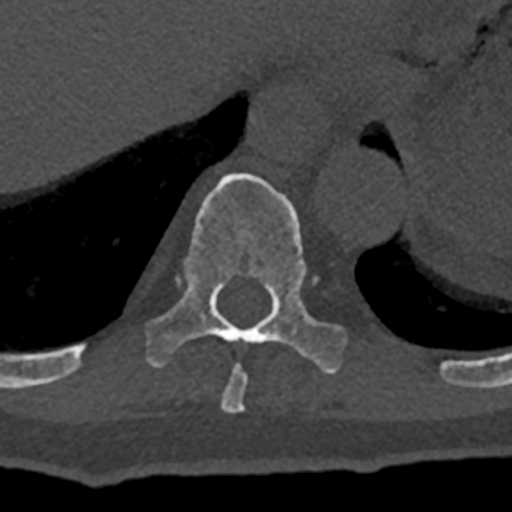
CT including the spine, one axial slice; slice 608 of 797 in the series (ordered by position); reconstruction kernel Br40s/3; 120 kVp; bone window (W 1800 / L 400 HU); 0.5 mm slice thickness; 512 × 512 image matrix, field of view 160 × 160 mm. Patient: male, 74 years. From the clinical record (not read from this slice): primary cancer: renal; vertebrae with lytic lesions (as recorded): T10, L1, L2, L3, L4, L5.
Structures marked on this image (semi-automatic segmentation, software-assisted and operator-edited):
- T10 vertebra: bounding box <70,173,347,374> (left, top, right, bottom; pixels)
- T9 vertebra: <220,365,247,413>